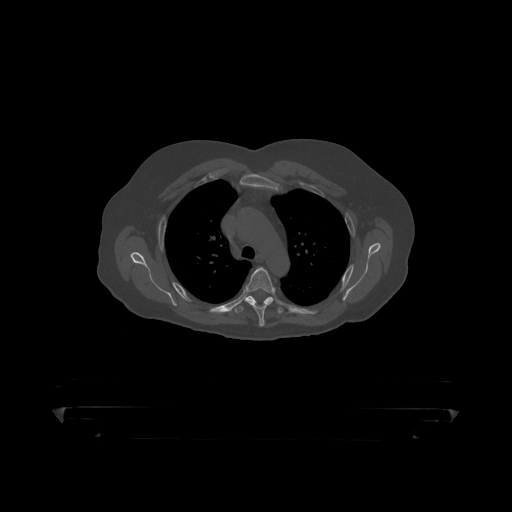
CT including the spine, one axial slice; position 333 of 390 along the scan axis; reconstruction kernel STANDARD; bone window (W 1800 / L 400 HU); 1.25 mm slice thickness; 512 × 512 image matrix, field of view 650 × 650 mm. Male patient, age 60 years. Case-level facts recorded for this patient, not image findings: primary cancer: prostate.
Structures marked on this image (semi-automatic segmentation, software-assisted and operator-edited):
- T4 vertebra: bounding box <245,268,276,319> (left, top, right, bottom; pixels)
- T5 vertebra: <234,296,285,315>